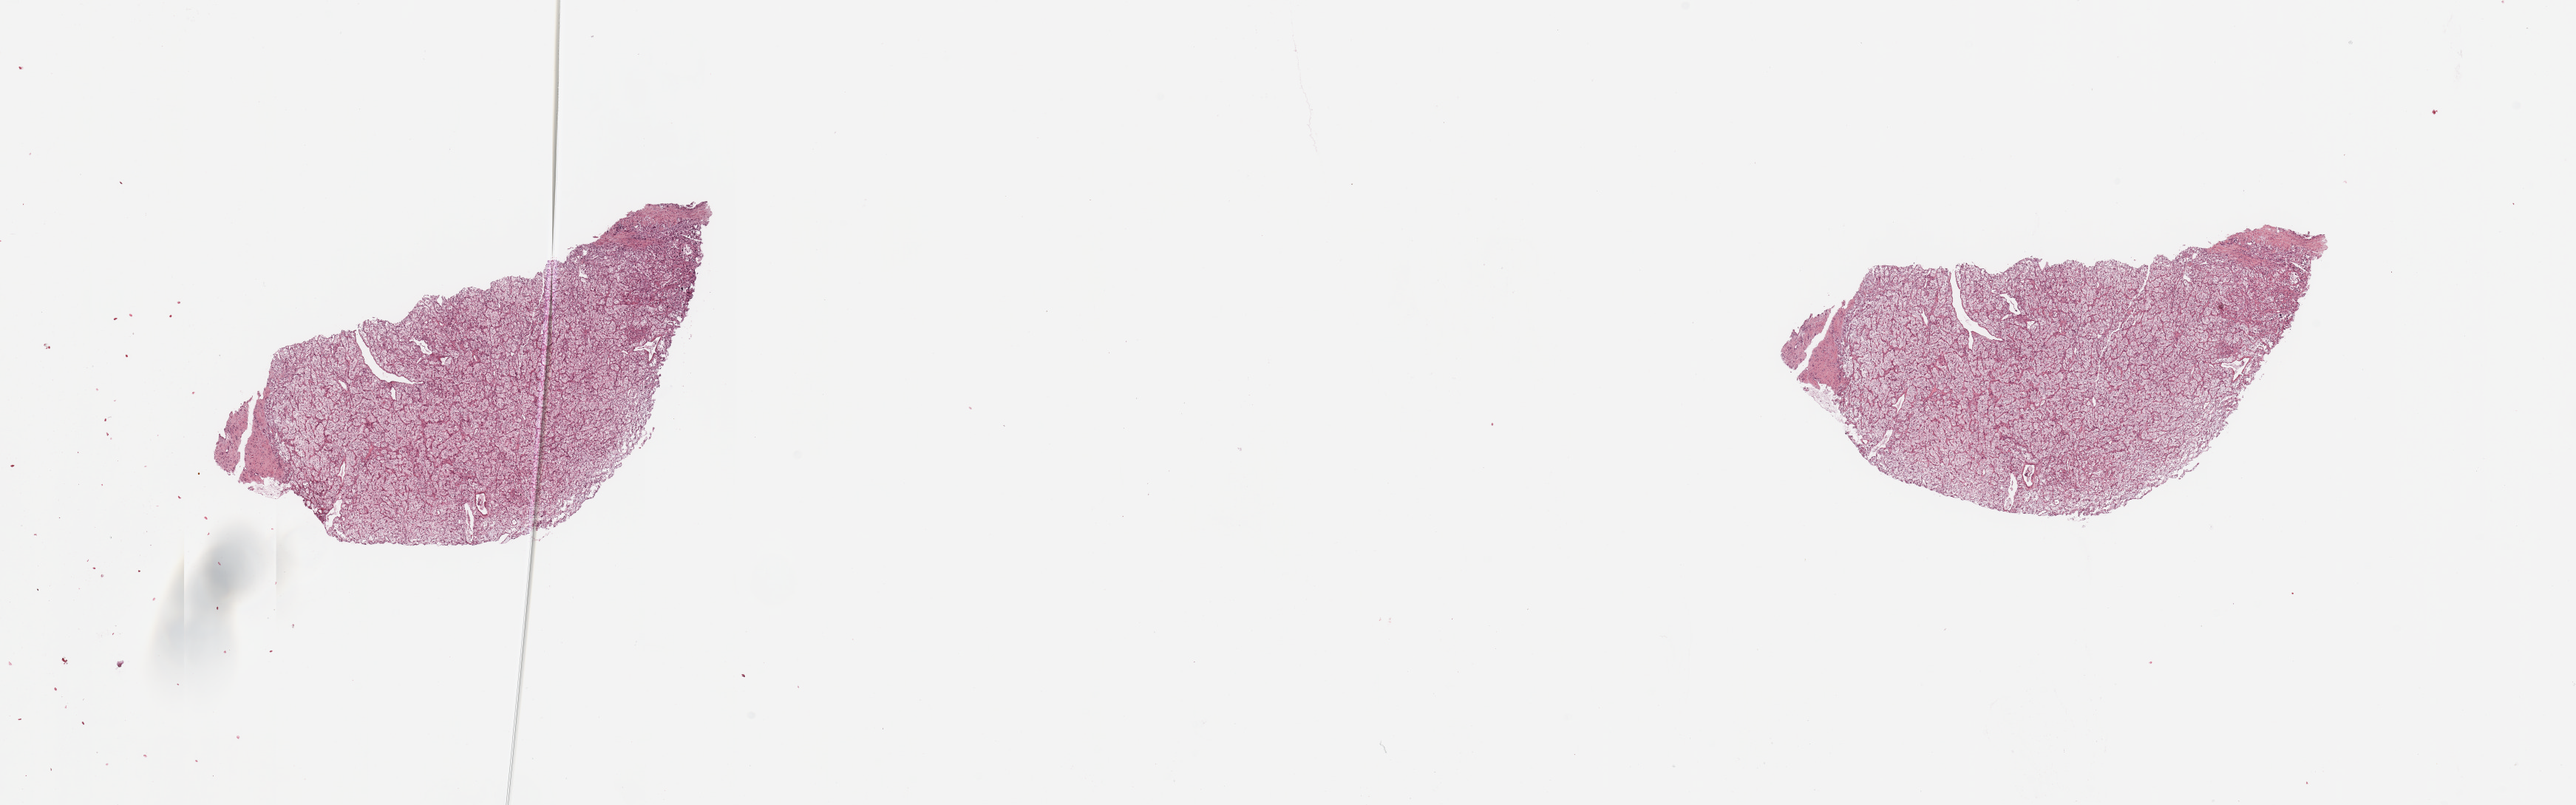
Hematoxylin and eosin (H&E) stained whole-slide image, shown as a low-resolution overview of the whole scanned area (about 27.6 x 8.6 mm). Tumour tissue sample, sampled site: kidney. Patient: male, age 59 years. Histologic grade: G2 (moderately differentiated). Pathologist review of this section (percent, as recorded): tumour nuclei 85%, necrosis 0%.
AJCC pathologic stage: III. Diagnosis: Renal cell carcinoma, NOS. Primary tumour site (as recorded): lower pole.